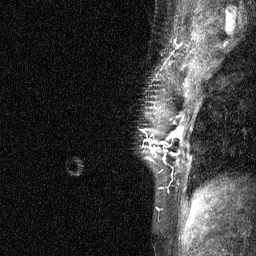
Breast MRI (dynamic contrast-enhanced), one sagittal slice; dynamic contrast-enhanced study with each time point stored as its own series, time point 3 of 4 at this slice position (ordered by acquisition time); 1.5 T; TE 4.8 ms, TR 27 ms; 256 × 256 image matrix. Patient: female, 44 years. From the clinical record (not read from this slice): setting: breast cancer imaged before/during neoadjuvant chemotherapy; receptor status: HR-positive, HER2-negative.
Annotated regions visible in this slice (semi-automatically segmented with operator editing):
- analysis volume of interest (the breast-tissue region the enhancement analysis was run in; not a lesion): bounding box <139,117,185,188> (left, top, right, bottom; pixels)
- tumour enhancement mask (voxels above the 90 % enhancement threshold inside the analysis volume of interest): <164,130,183,154>